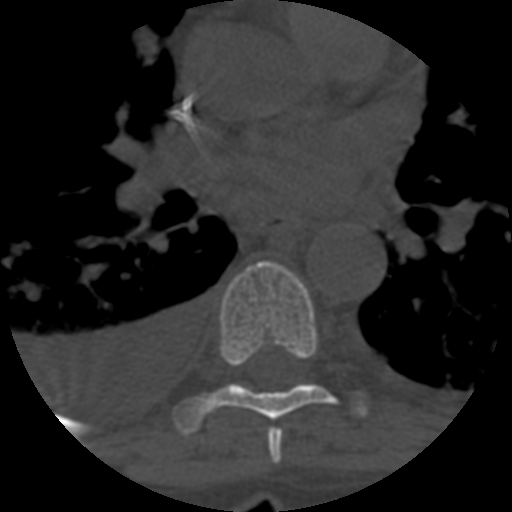
CT including the spine, one axial slice. Slice 416 of 708 in the series (ordered by position). Reconstruction kernel STANDARD. 120 kVp. One of 3 acquisitions stored at this slice position. Bone window (W 1800 / L 400 HU). 512 × 512 image matrix. Patient age 55 years. From the clinical record (not read from this slice): primary cancer: colon.
Structures marked on this image (semi-automatic segmentation, software-assisted and operator-edited):
- T6 vertebra: box from (x=267, y=428) to (x=283, y=464) px
- T7 vertebra: (x=174, y=261)–(x=336, y=434)